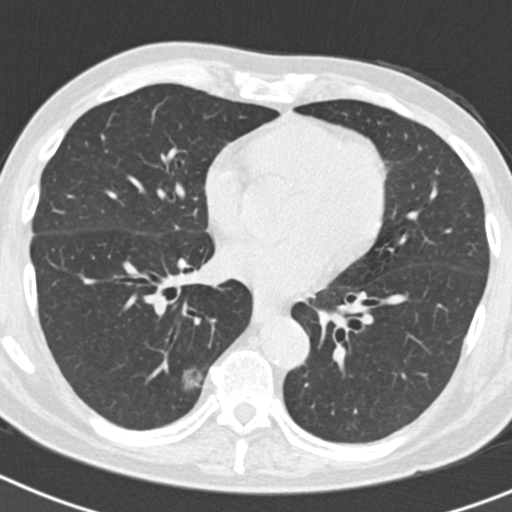
Chest CT (low-dose screening protocol), one axial image. Second annual screen. Lung window (W 1500 / L -600 HU). 512 × 512 image matrix. Male, age 70 years at enrolment.
• Lesion marked by an expert reader, bounding box (x1, y1, x2, y2) in pixels: (124, 357, 209, 429).
• The screening reader recorded 5 non-calcified nodules or masses ≥4 mm on this exam; which of them this box marks is not recorded.
• Official screen result: positive, other.
• Participant outcome: lung cancer diagnosed 622 days after this screen (after the third annual screen) — bronchiolo-alveolar adenocarcinoma, NOS, right lower lobe, poorly differentiated (G3), stage IB (AJCC 6th edition), 30 mm at pathology.